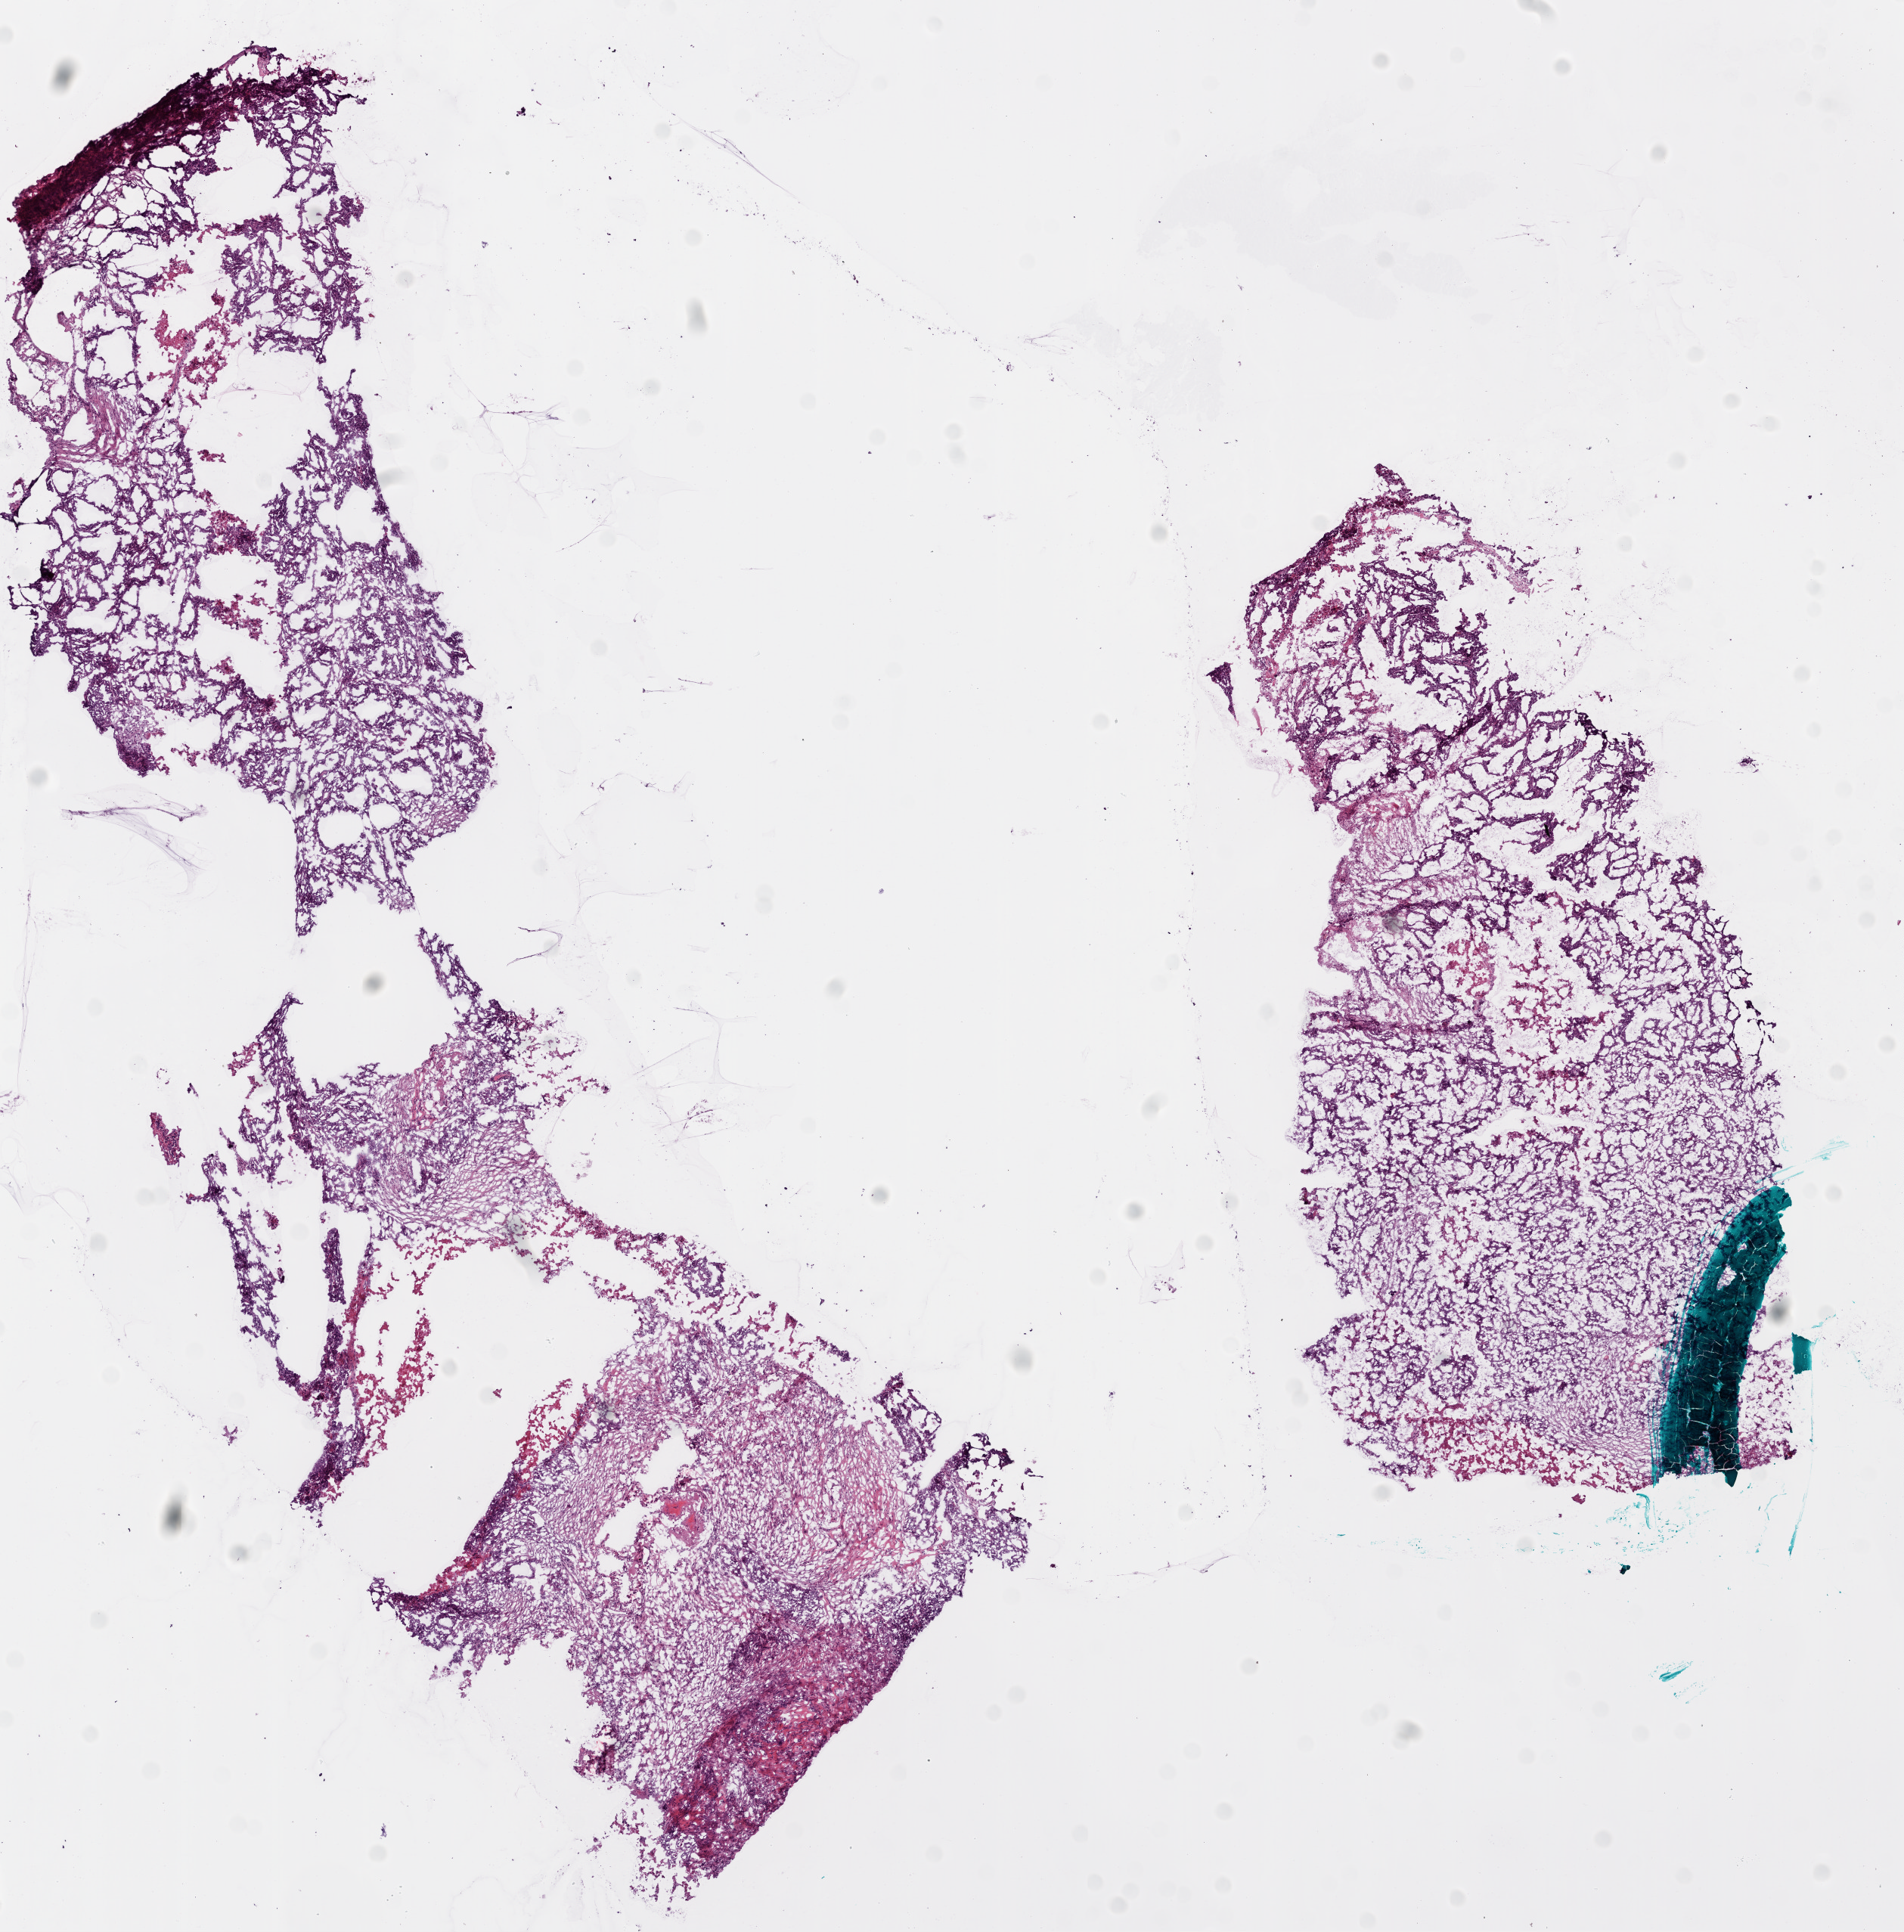
Whole-slide histology image, H&E-stained, low-resolution overview of the scanned area, about 10.2 x 10.3 mm, frozen section from the bottom of the tissue portion, ovary, primary tumour sample. Female, age 85 years at initial diagnosis. Histologic grade: G3 (poorly differentiated). Composition of this section per pathologist review: tumour cells 55%, tumour nuclei 80%, stromal cells 28%, necrosis 17%.
Diagnosis: Serous cystadenocarcinoma, NOS.